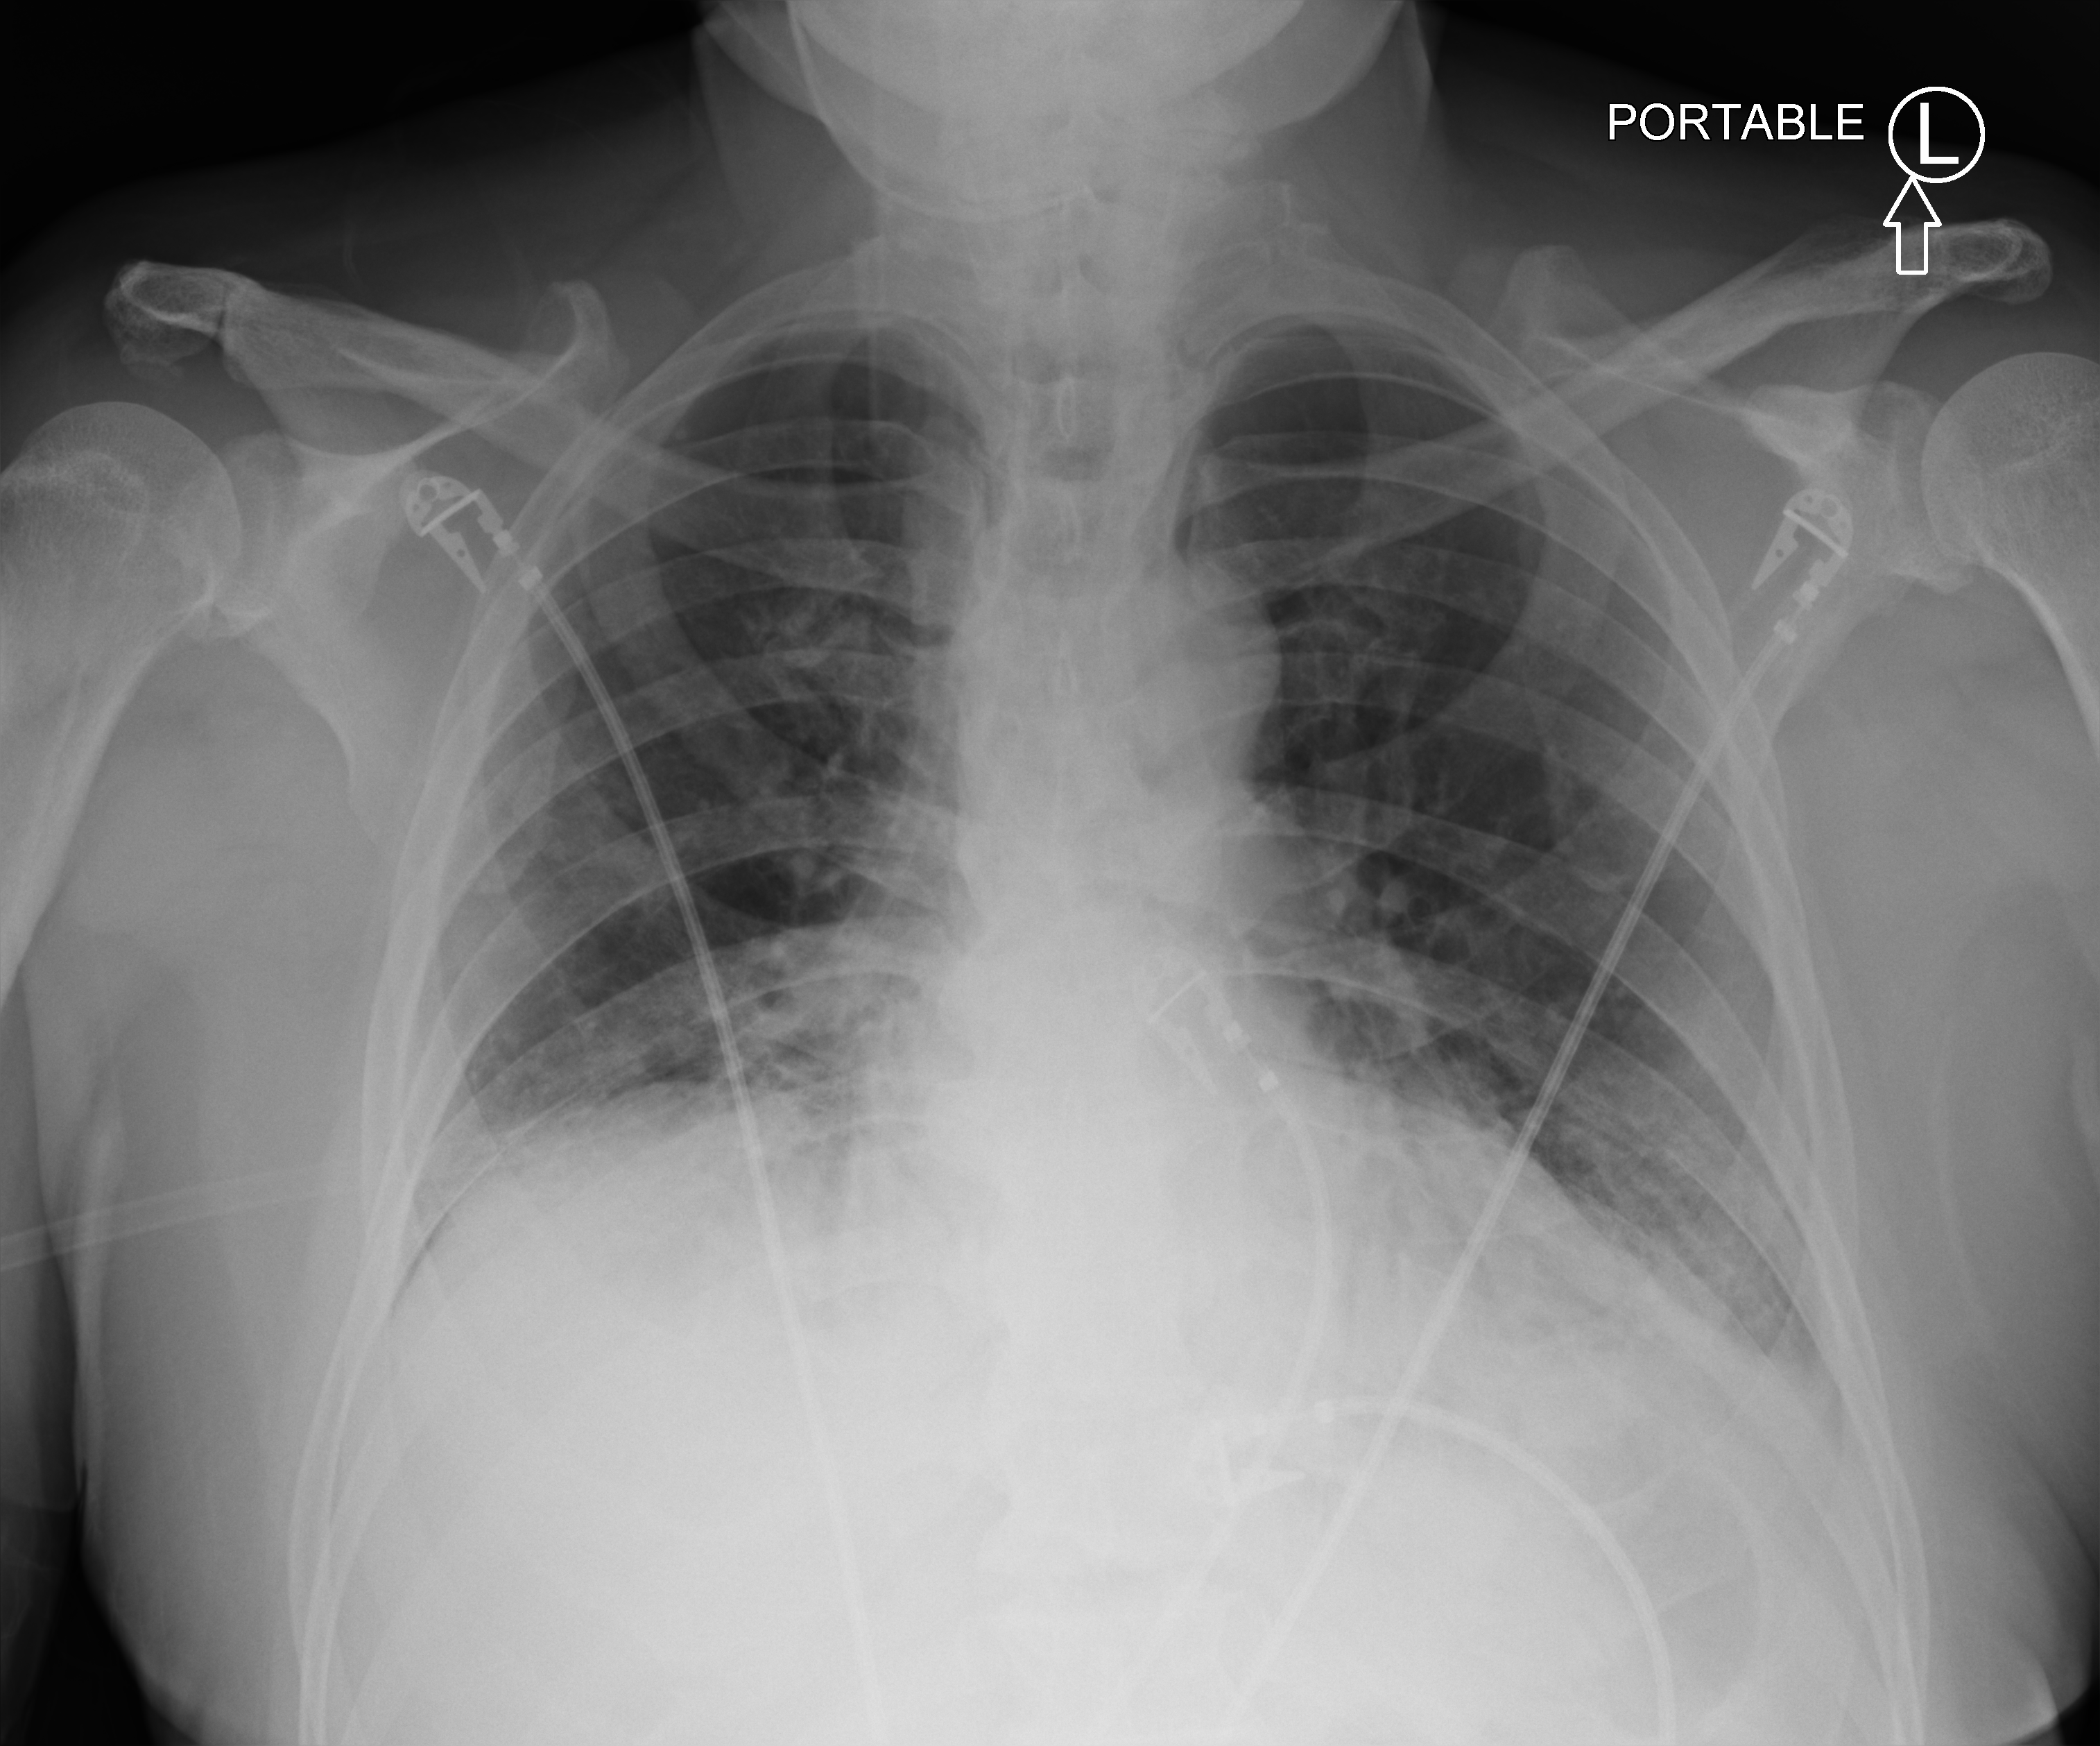
Portable chest radiograph; anteroposterior (AP) projection. Patient hospitalised with COVID-19; male, aged 75–90 years.
Hospital-stay facts (about this admission, not read from this image; timing relative to this image not recorded):
- mechanically ventilated during this hospital stay: yes